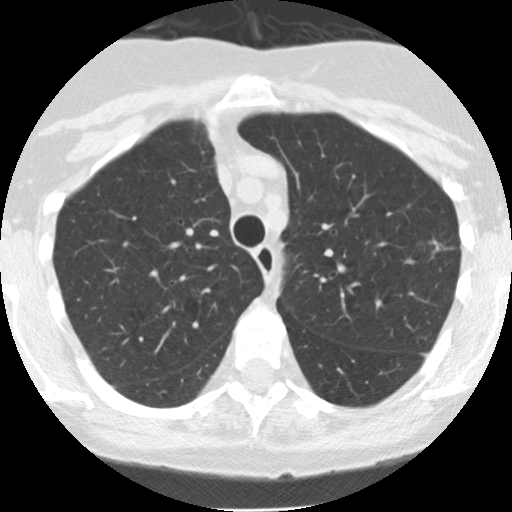
Low-dose screening chest CT, one axial slice; slice 111 of 145 in the series (ordered by position); reconstruction kernel STANDARD; lung window (W 1500 / L -600 HU); 2.5 mm slice thickness; 512 × 512 image matrix.
Annotated regions visible in this slice (expert manual segmentation):
- lesion 1 (tumor, upper lobe of left lung): bounding box (x1, y1, x2, y2) in pixels: (433, 240, 440, 252)